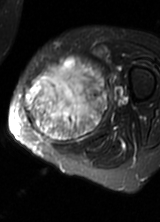
MRI of an extremity soft-tissue mass, one axial slice; position 26 of 69 along the scan axis; T2-weighted fat-saturated; MR volume resampled by the dataset authors to the PET/CT grid (not the native acquisition matrix); 3.27 mm slice thickness; 160 × 222 image matrix, field of view 156 × 217 mm. Female patient. From the clinical record (not read from this slice): histological type: pleomorphic leiomyosarcoma; grade: high; site of the primary tumour: left thigh.
Annotated regions visible in this slice (expert contour drawn on MRI and transferred to this co-registered scan by the dataset authors):
- gross tumour volume including surrounding oedema: box from (x=23, y=59) to (x=110, y=144) px
- gross tumour volume (mass): (x=23, y=61)–(x=108, y=144)